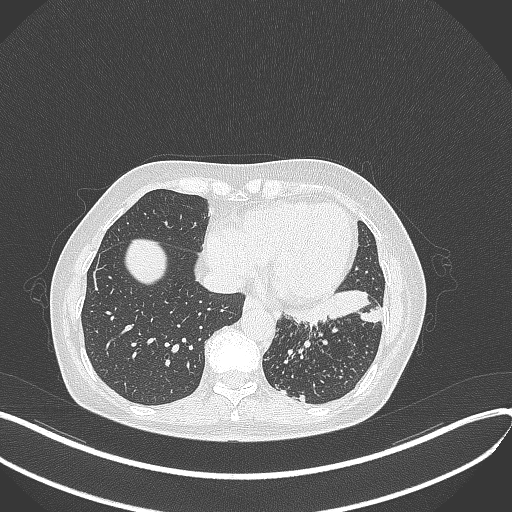
Chest CT, one axial slice; slice 124 of 429 in the series (ordered by position); reconstruction kernel B70f; 100 kVp; lung window (W 1500 / L -600 HU); 1 mm slice thickness; 512 × 512 image matrix, field of view 400 × 400 mm. Patient: female, 63 years. From the clinical record (not read from this slice): clinical TNM (as recorded): T1b N0 M0; histopathological grade: G2-3.
Structures marked on this image (rectangle marked by the reading radiologist):
- lung tumour (recorded histology: adenocarcinoma): bounding box <282,289,383,331> (left, top, right, bottom; pixels)